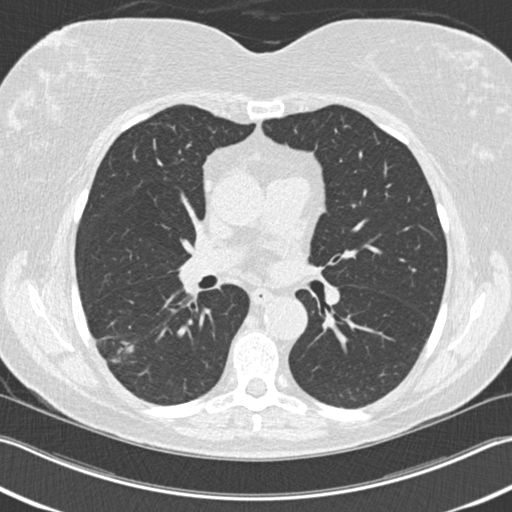
Low-dose screening chest CT, axial slice; baseline screening round; lung window (W 1500 / L -600 HU); 2 mm slice thickness; standard (soft-tissue) reconstruction kernel (B30f); slice 85 of 211 in the series. Female participant, aged 63 years at enrolment.
Lesion marked by an expert reader, bounding box (x1, y1, x2, y2) in pixels: (90, 322, 148, 373). The screening reader recorded 3 non-calcified nodules or masses ≥4 mm on this exam (right upper lobe, right lower lobe, right lower lobe); which of them this box marks is not recorded. Official screen result: positive, change unspecified: nodule(s) >= 4 mm or enlarging nodule(s), mass(es), or other non-specific abnormalities suspicious for lung cancer.